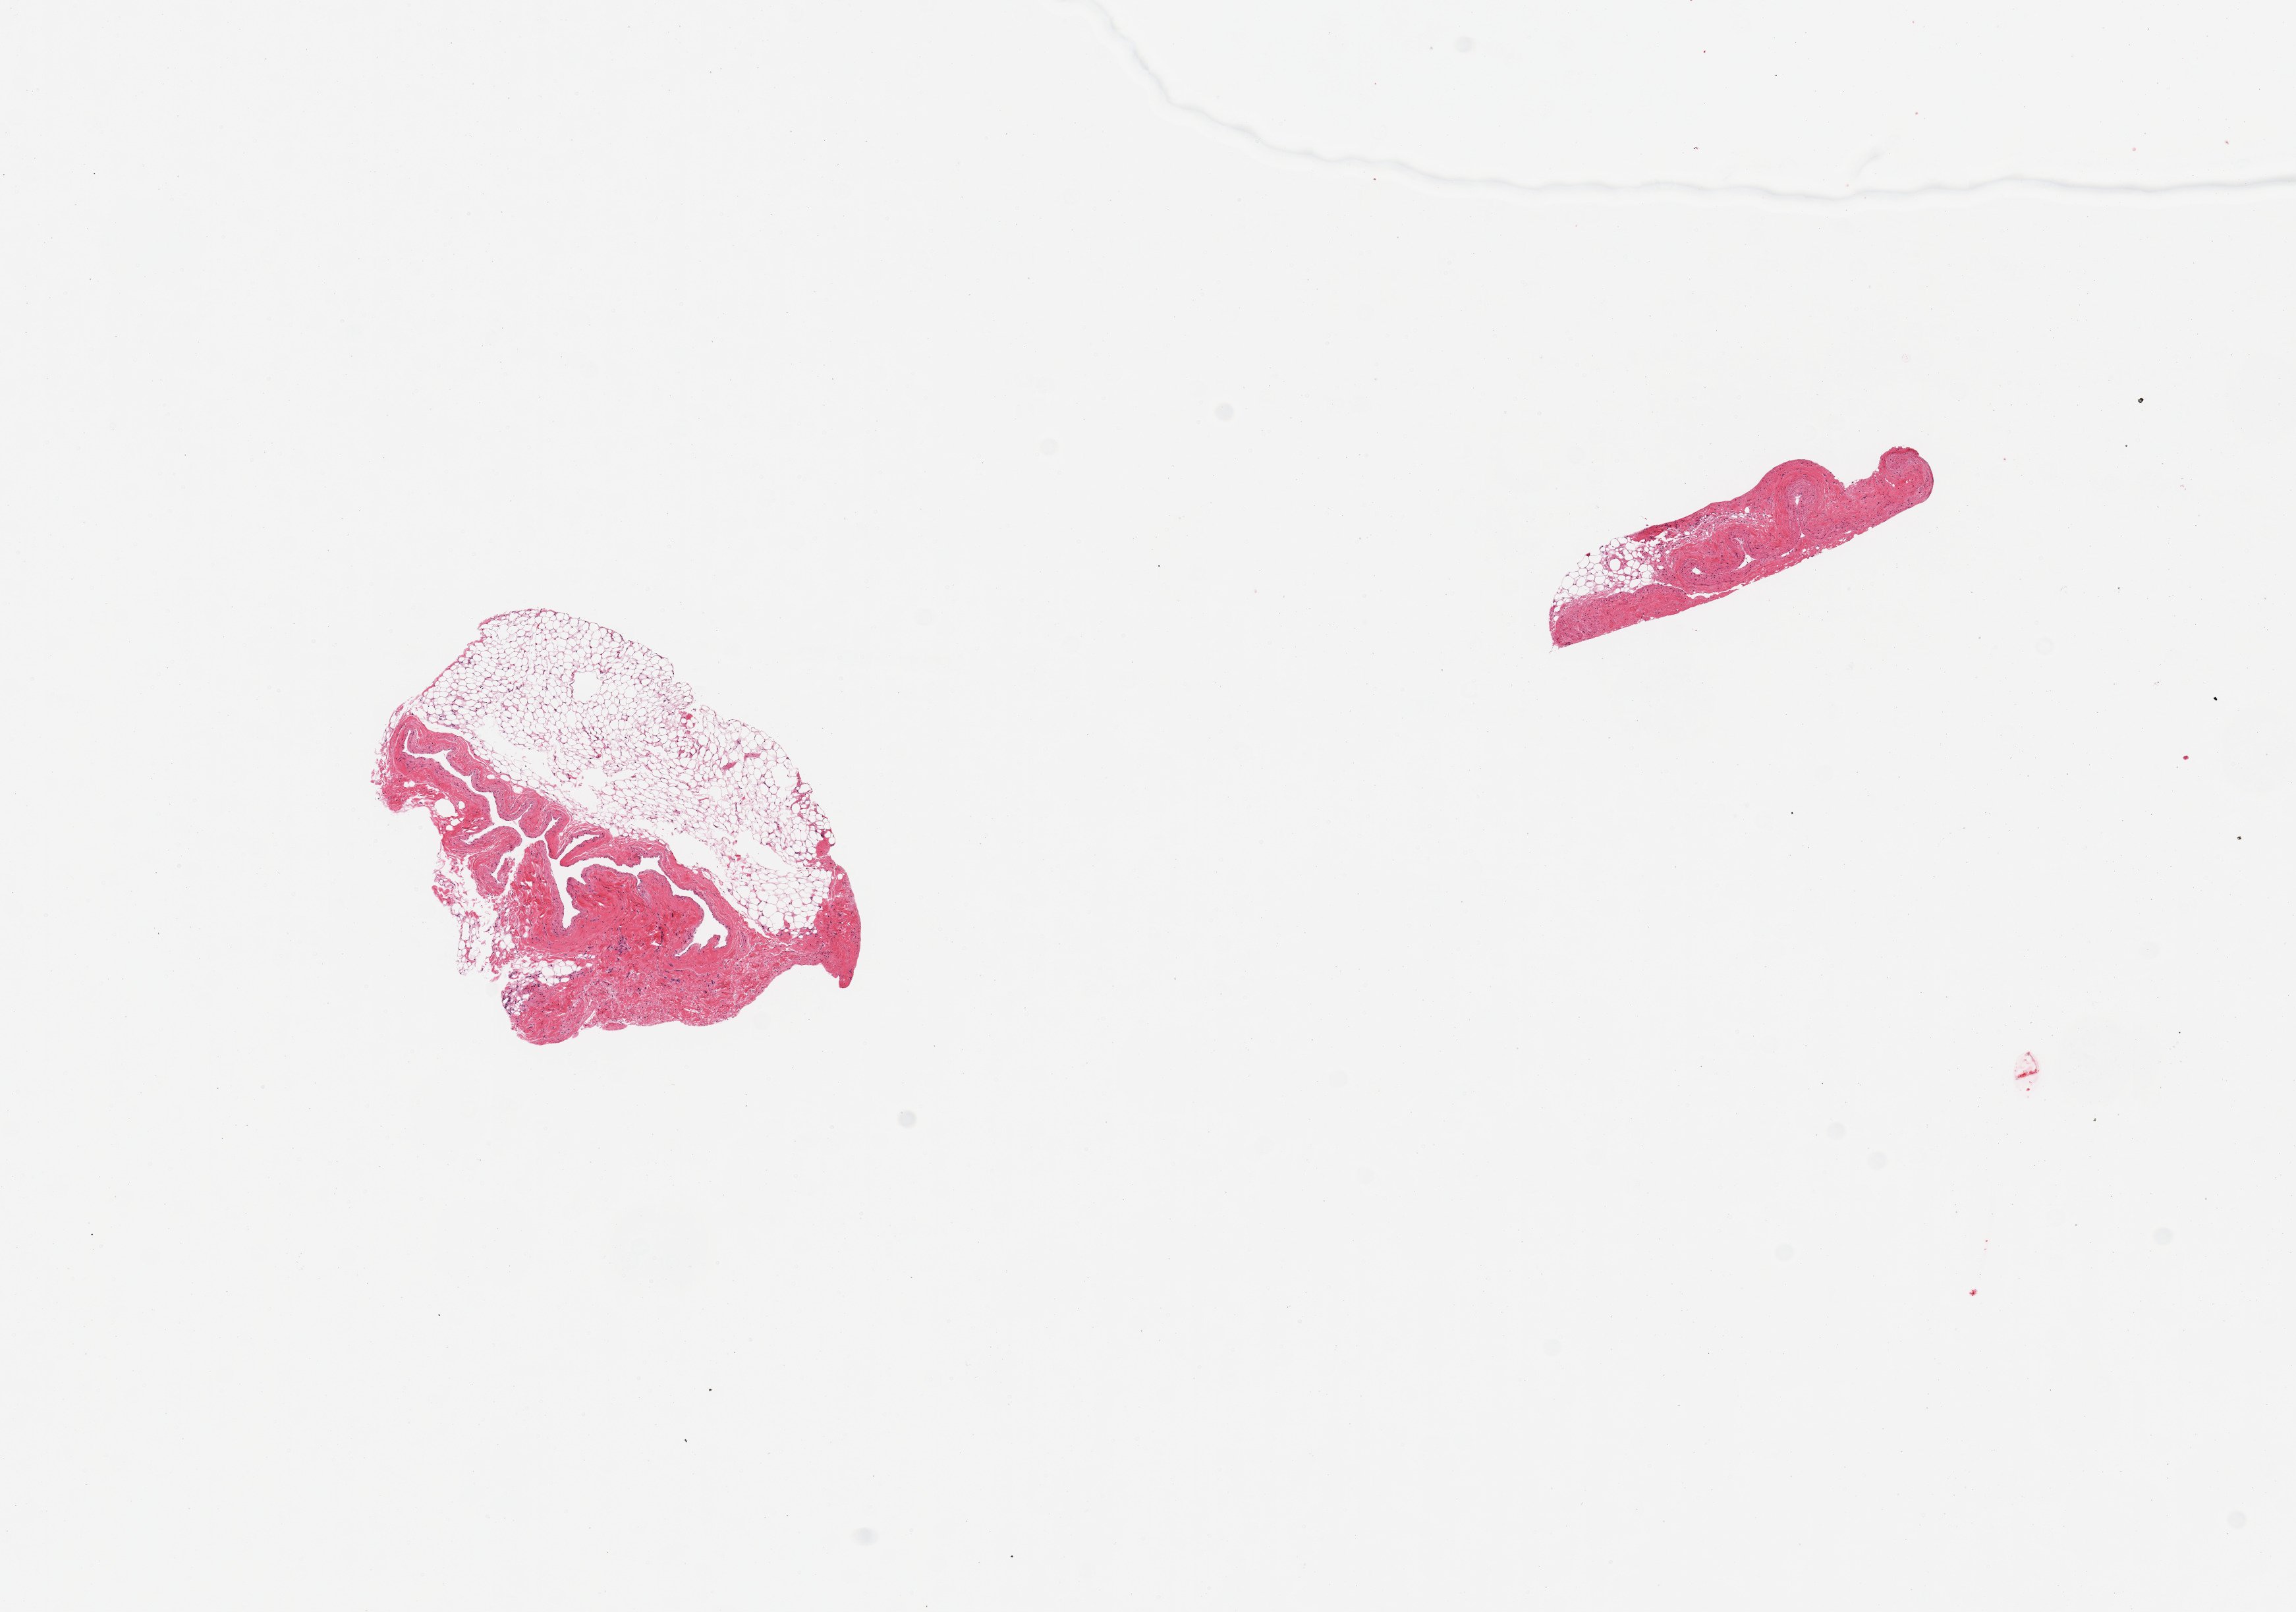
Digitized hematoxylin and eosin (H&E)-stained section — low-resolution overview of the scanned area, about 13.8 x 9.7 mm (acquisition: 20x scan); PAXgene-fixed paraffin-embedded (PFPE) section; sampled site (target tissue): coronary artery; tissue donor sample. Donor sex: male.
Review note (as recorded): 2 pieces; vein and fat.